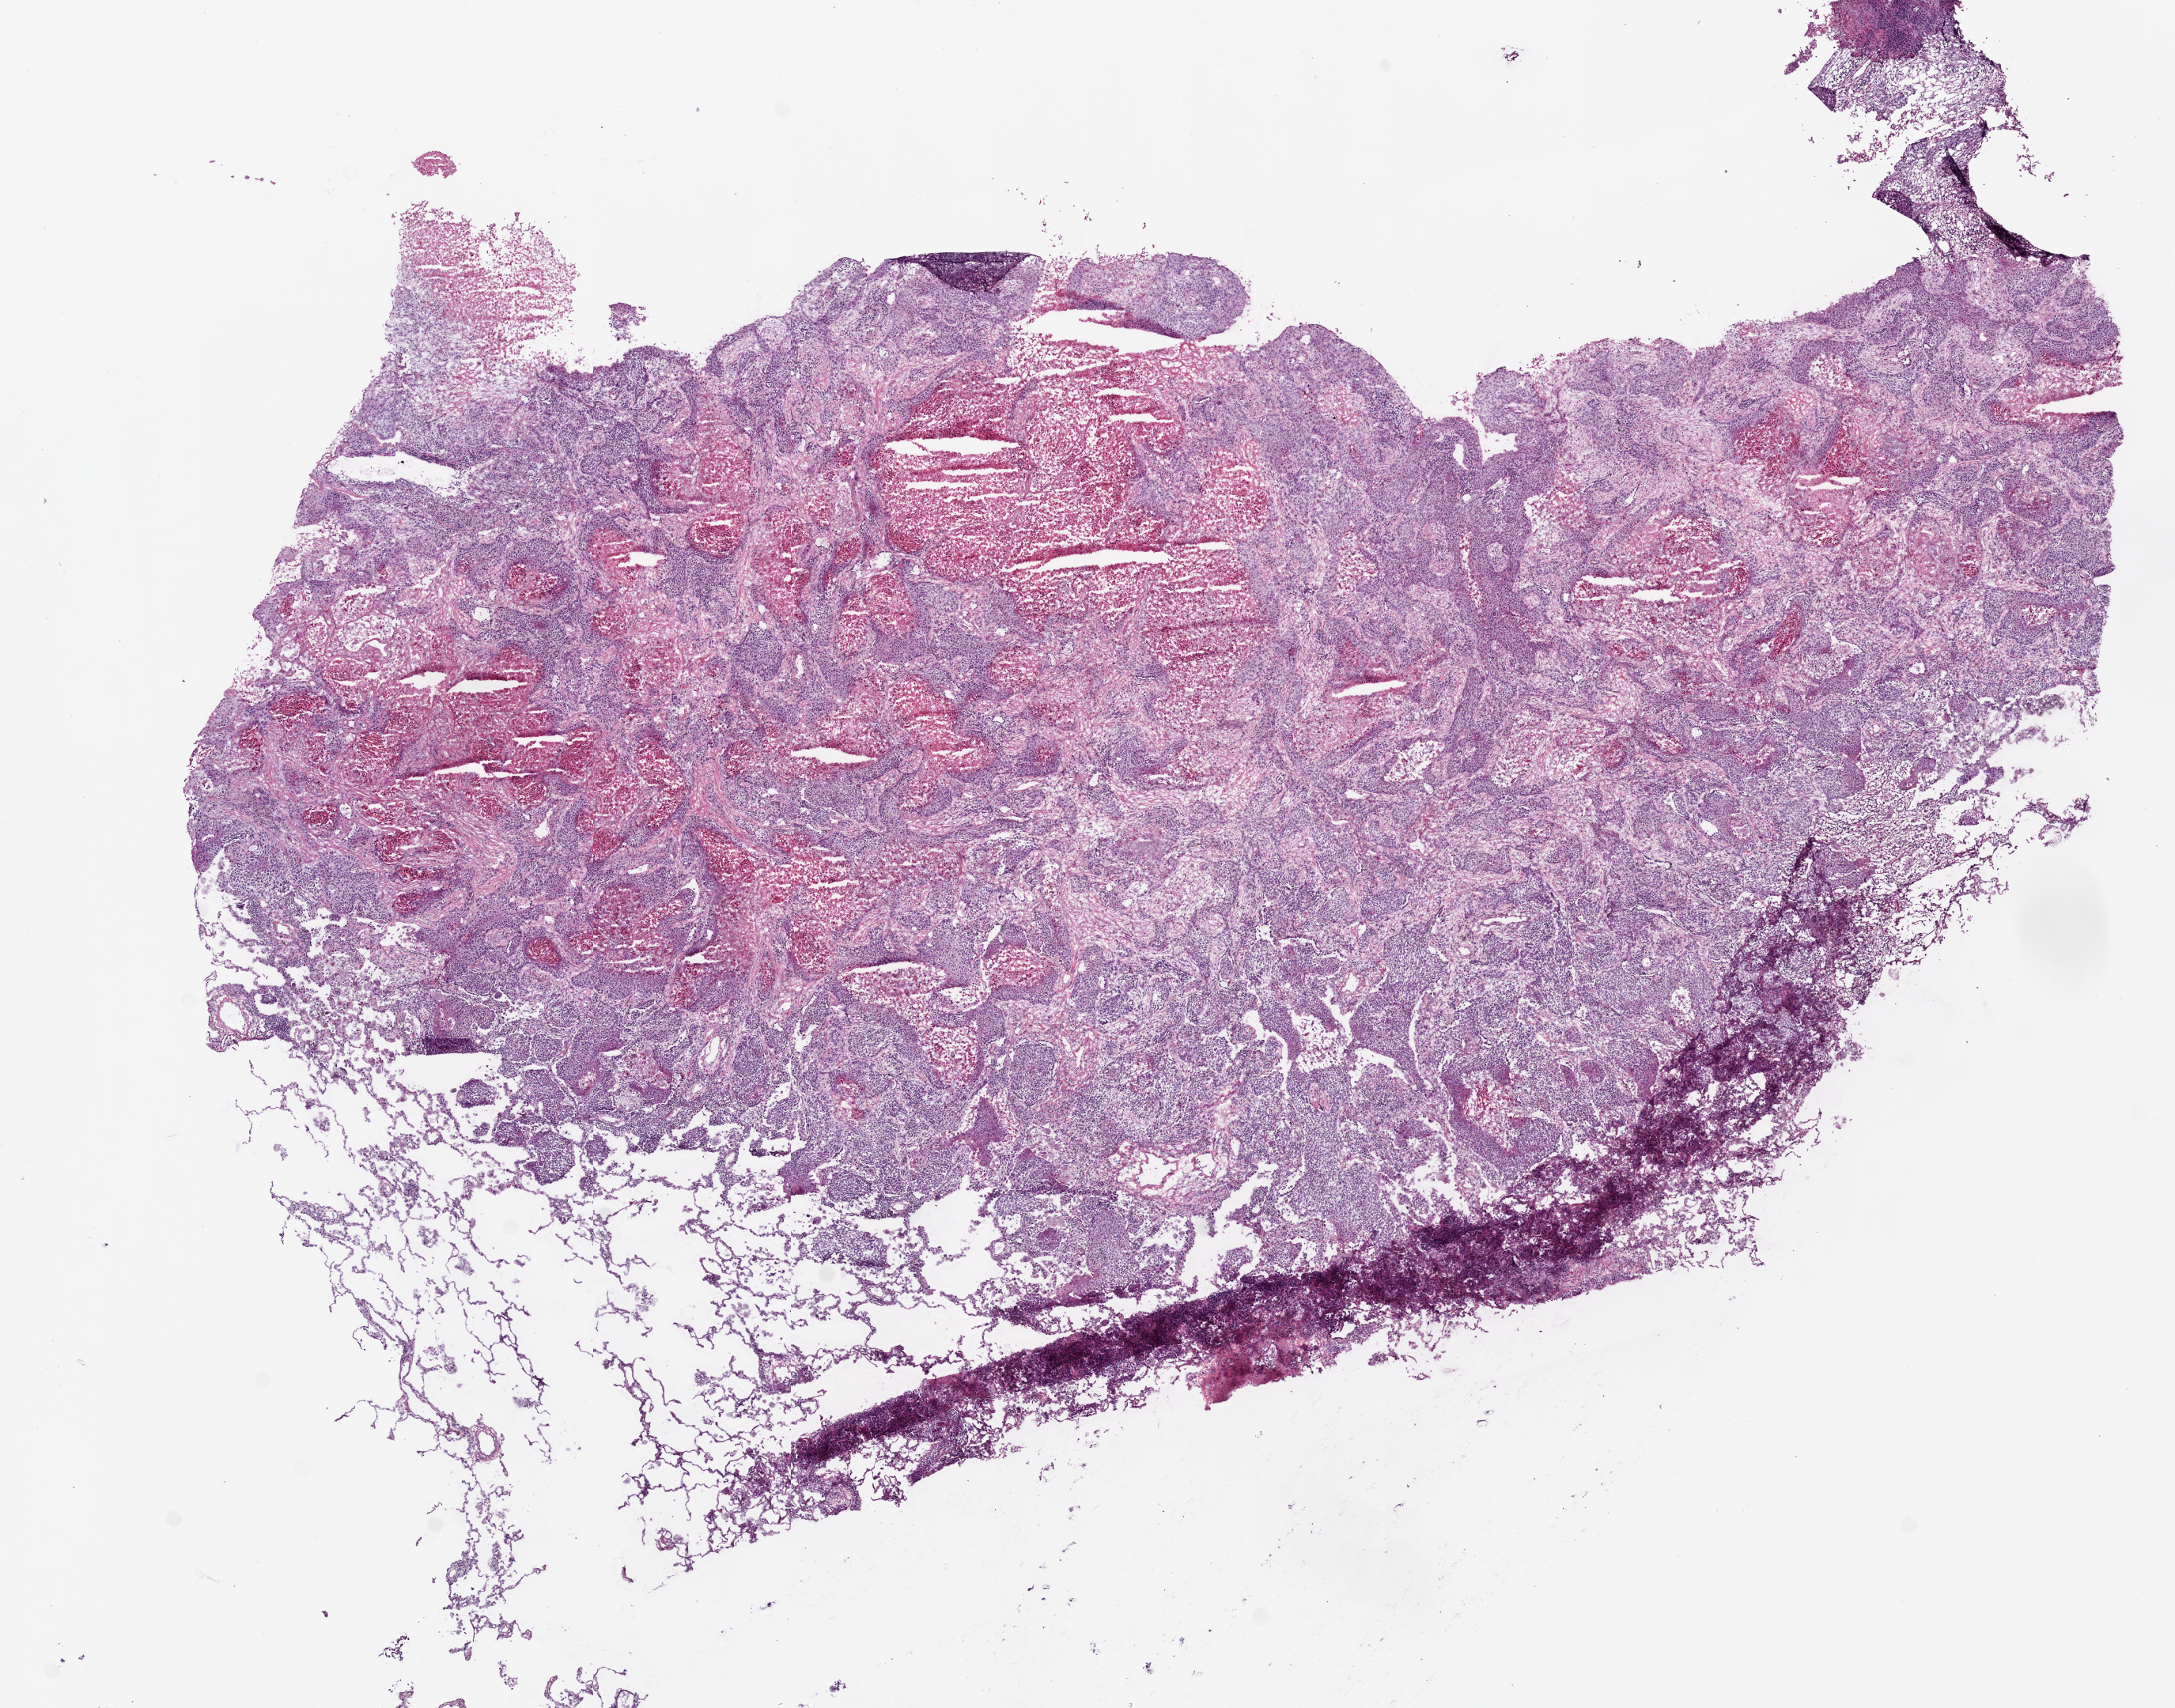
Whole-slide histology image, Hematoxylin and eosin (H&E) stained — shown as a low-resolution overview of the whole scanned area (about 11.0 x 8.7 mm), frozen section, sample: primary tumour, lung. Male, age 81 years at initial diagnosis. Slide review estimates, as recorded: tumour cells 30%, tumour nuclei 80%, normal cells 20%, stromal cells 10%, necrosis 40%.
AJCC pathologic stage: IA (6th edition). Histologic diagnosis: Squamous cell carcinoma, NOS (upper lobe, lung). TNM: T1 N0 M0.